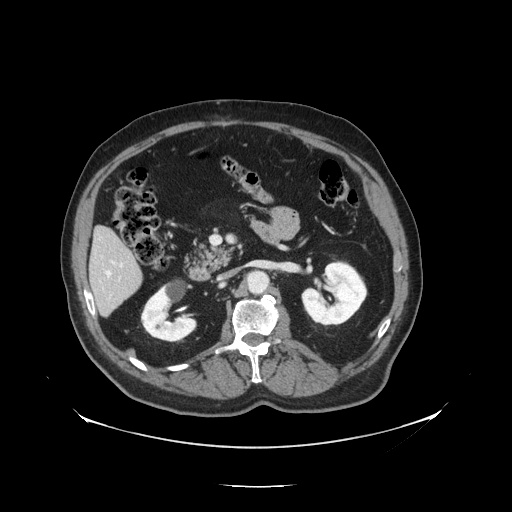
Contrast-enhanced abdominal CT, one axial slice. Slice 57 of 138 in the series (ordered by position). Reconstruction kernel STANDARD. 120 kVp. Intravenous contrast given. Soft-tissue window (W 400 / L 40 HU). 2.5 mm slice thickness. 512 × 512 image matrix. Male patient, age 77 years. From the clinical record (not read from this slice): diagnosis: colorectal cancer liver metastases, imaged before liver resection.
Outlined on this slice (expert manual segmentation):
- liver: box from (x=91, y=229) to (x=142, y=315) px
- planned liver remnant (the part of the liver to remain after resection): (x=92, y=229)–(x=139, y=283)